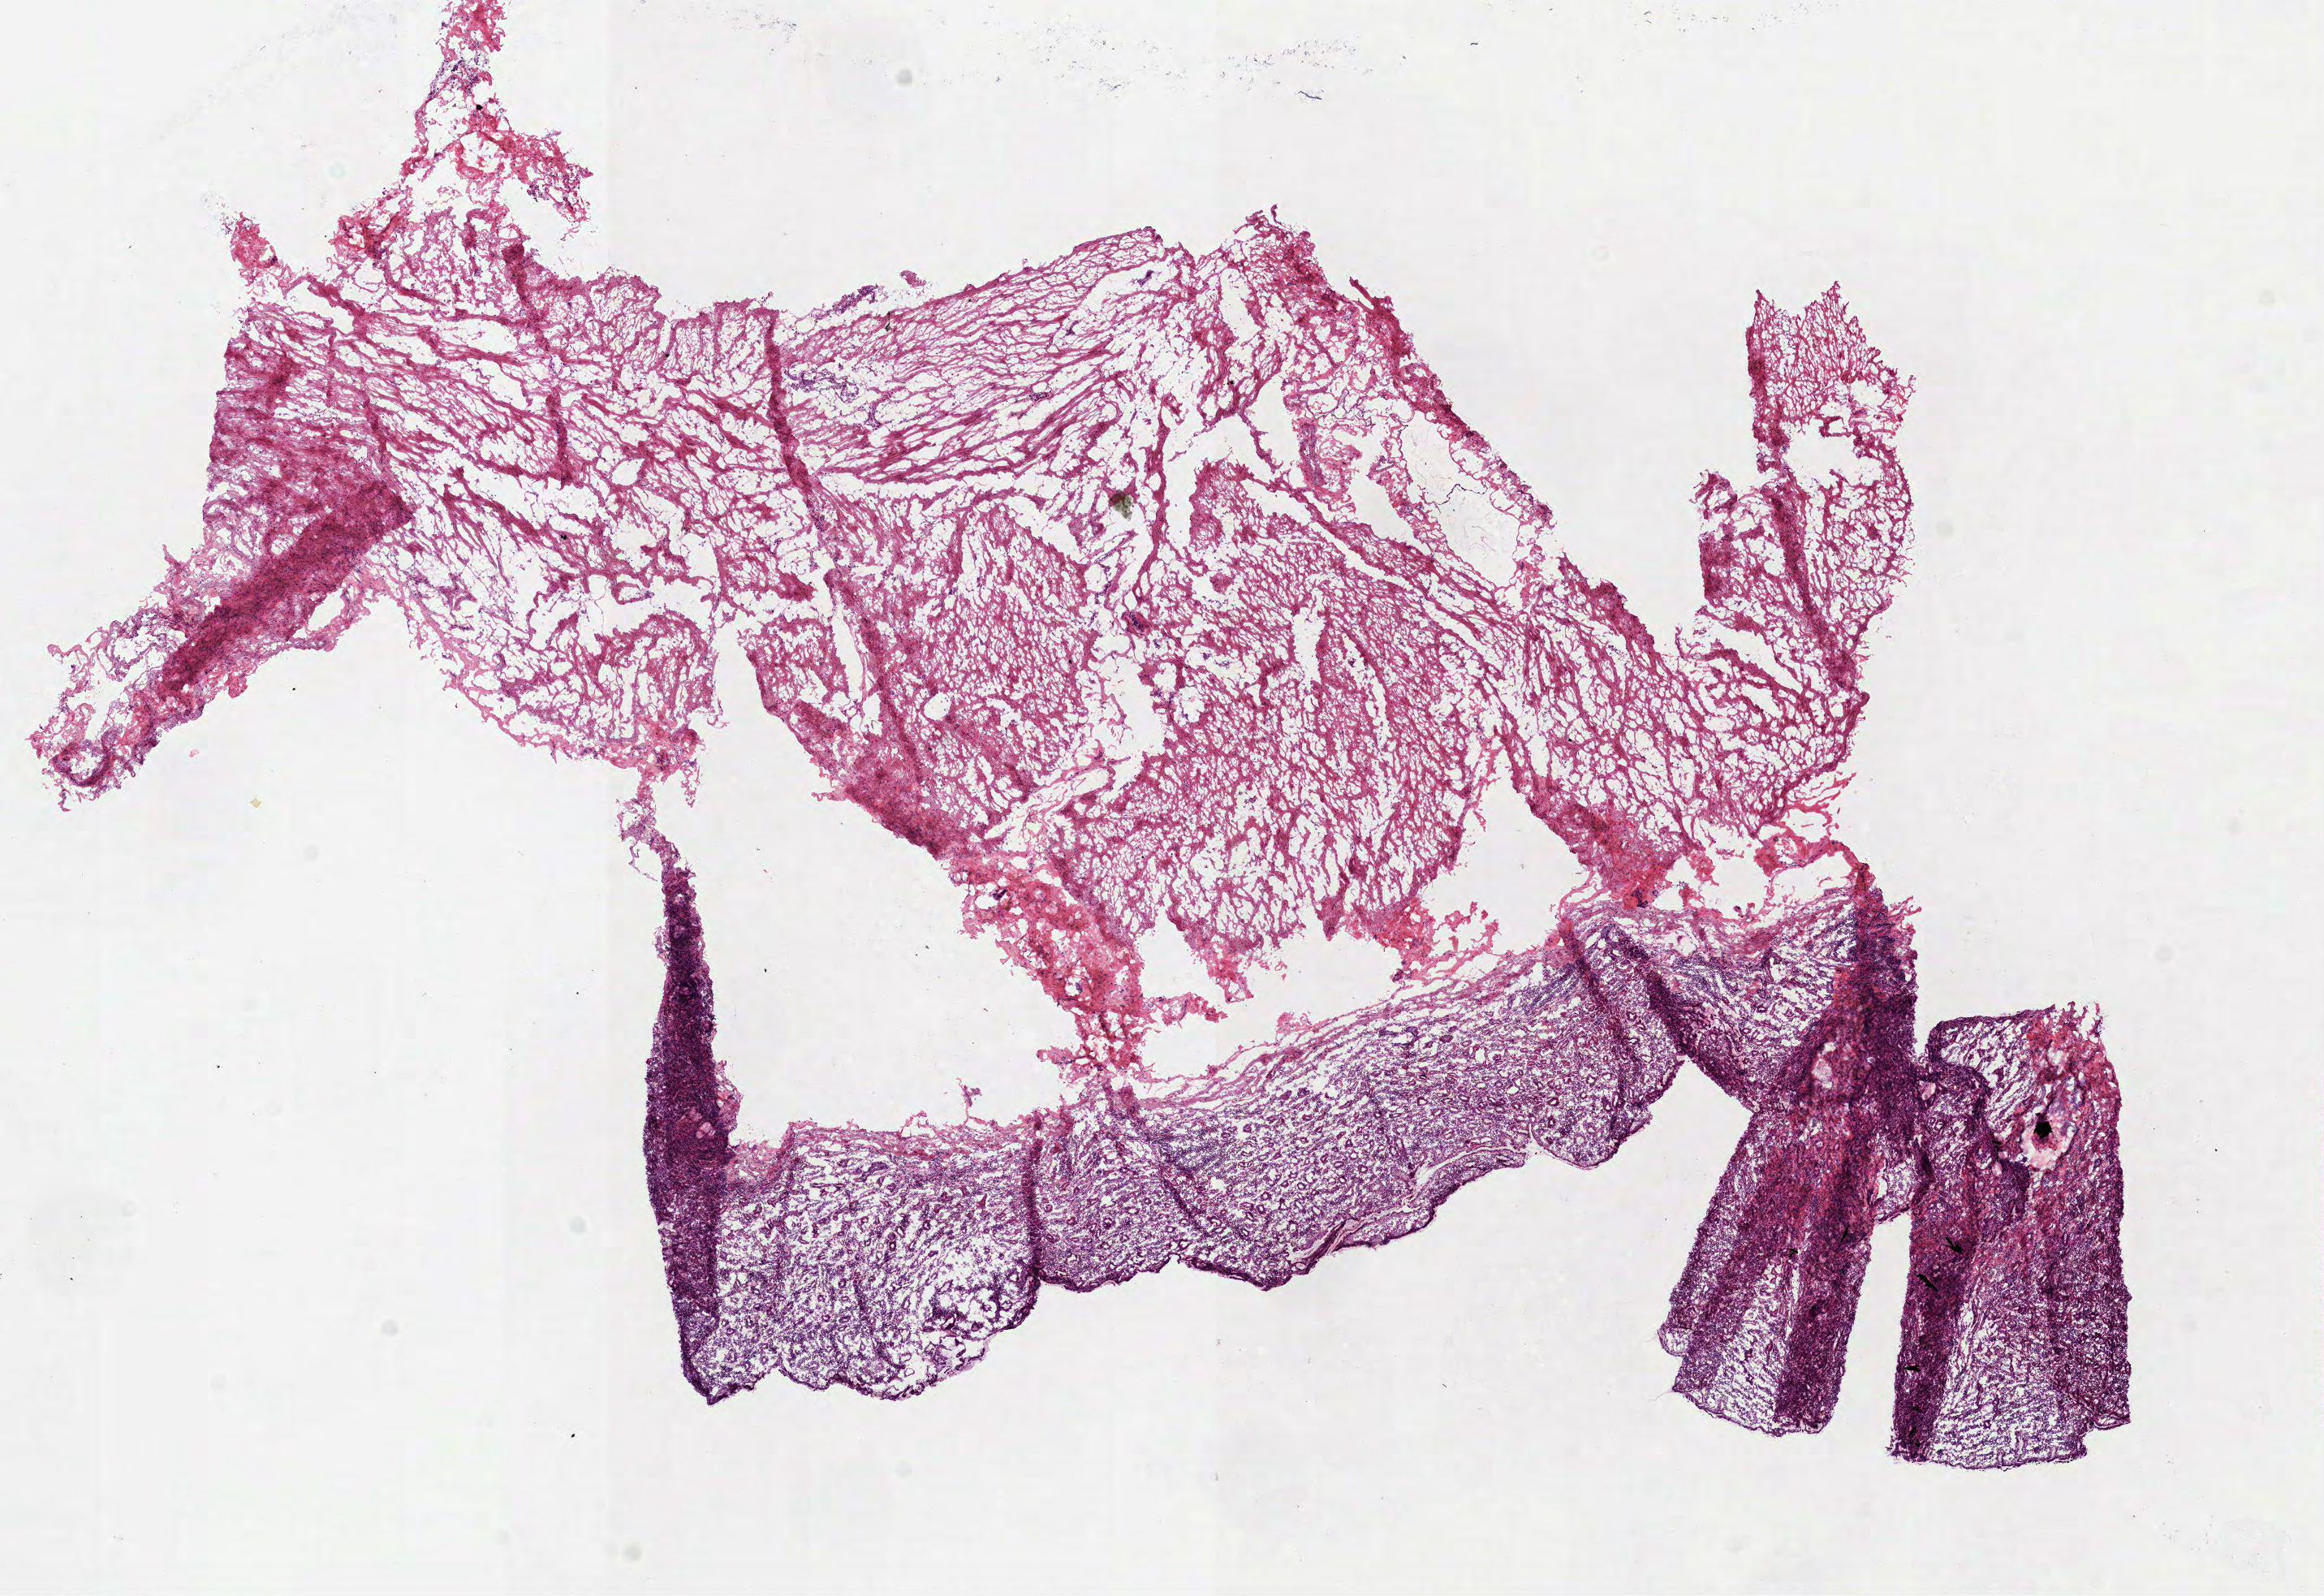
Digitized H&E-stained tissue section (whole slide), a low-resolution overview of the entire scanned area, about 11.5 x 7.9 mm (acquisition: 40x scan). Frozen section. Sample: solid tissue normal (non-tumour tissue), stomach. Female patient; age at initial diagnosis 78 years.
This section: solid tissue normal sample (biorepository sample class). Patient diagnosis: Adenocarcinoma, NOS (body of stomach).